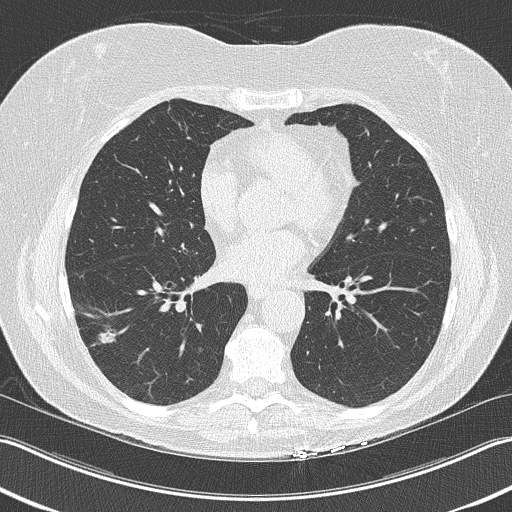
Low-dose screening chest CT, one axial slice; slice 105 of 210 in the series (ordered by position); 120 kVp; lung window (W 1500 / L -600 HU); 2 mm slice thickness; 512 × 512 image matrix, field of view 348 × 348 mm.
Annotated regions visible in this slice (outlined manually by an expert reader):
- lesion 1 (tumor, lower lobe of right lung): bounding box <99,330,117,344> (left, top, right, bottom; pixels)